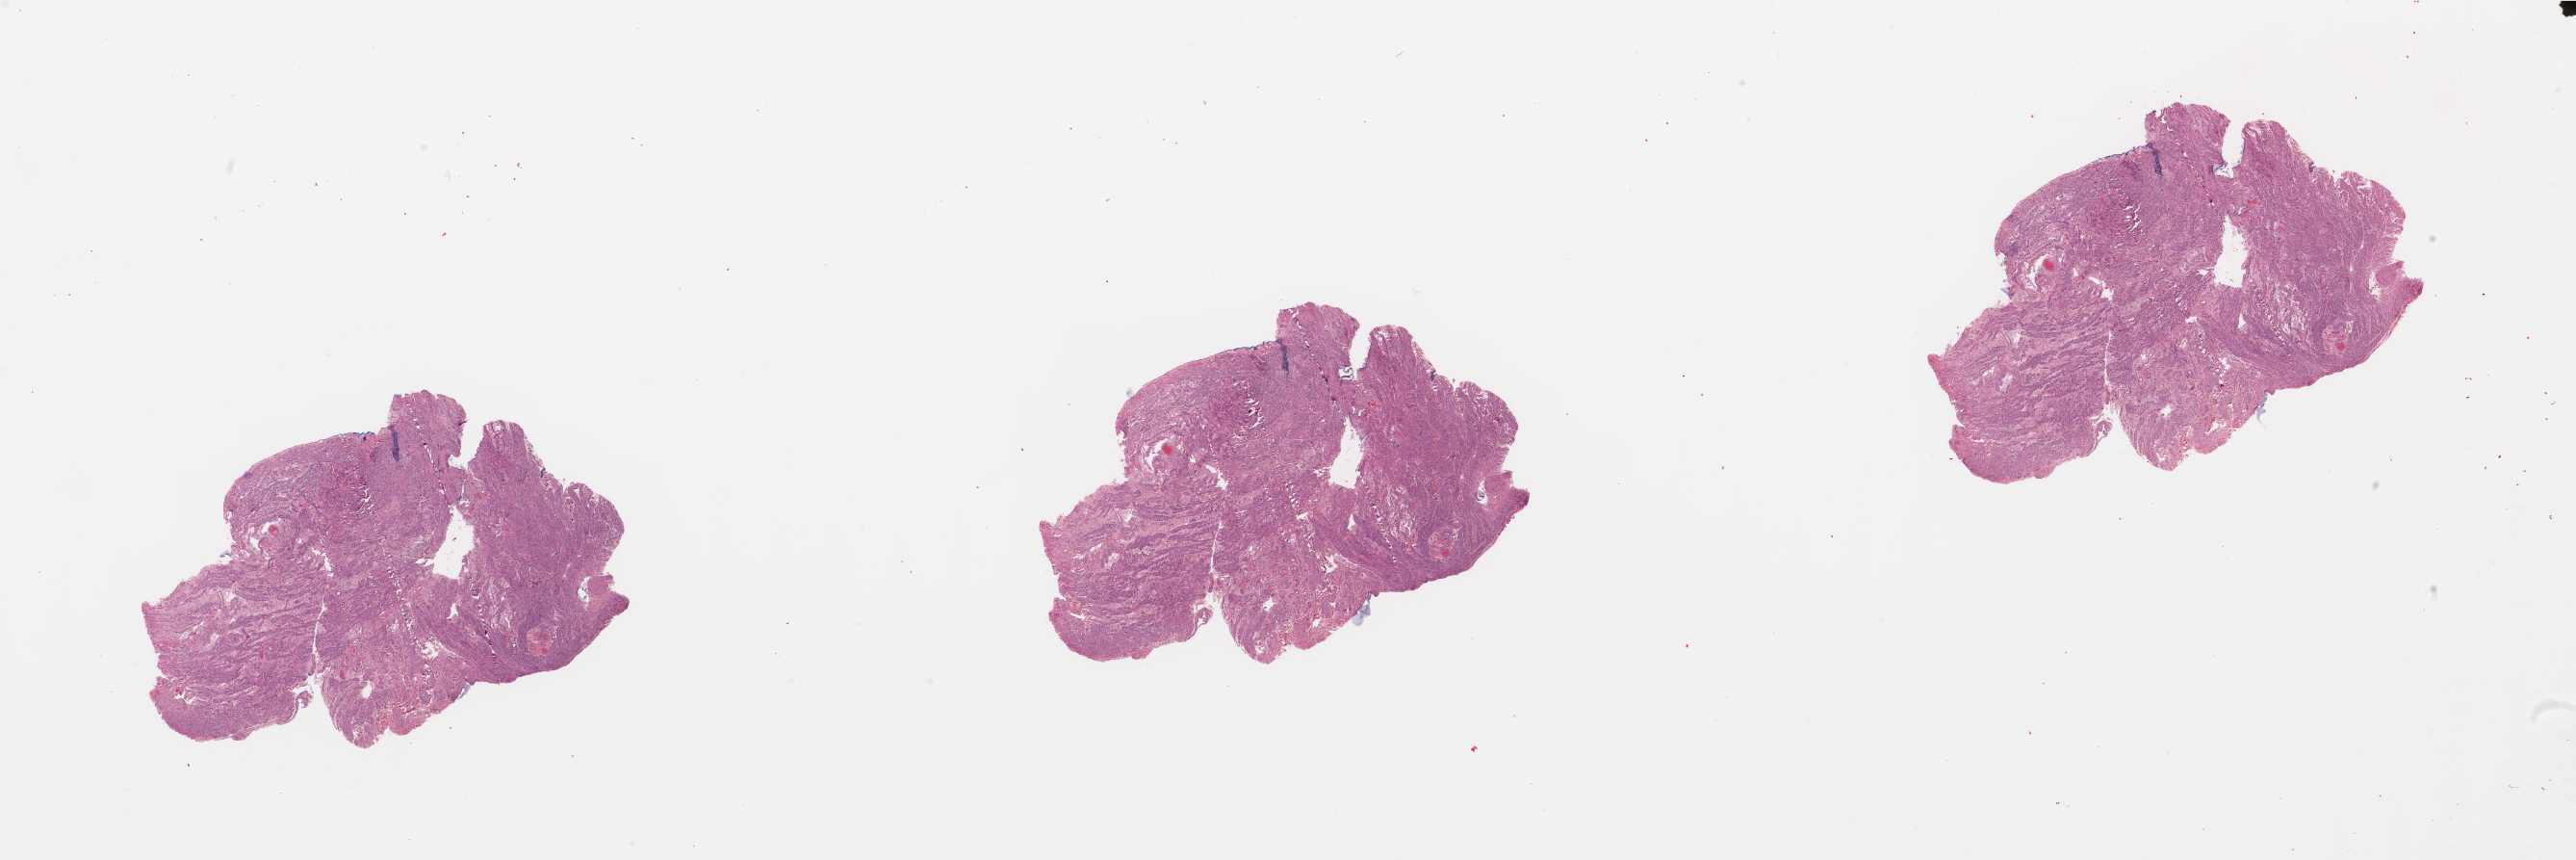
Whole-slide histology image, H&E — shown as a low-resolution overview of the whole scanned area (about 42.3 x 14.1 mm, from a 20x scan); normal (non-tumour) tissue sample, uterus. Patient: female, age 72 years.
* this section: normal (non-tumour) tissue from the same patient
* patient diagnosis: Endometrioid adenocarcinoma, NOS